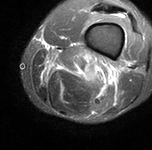
MRI of an extremity soft-tissue mass, one axial slice. Position 19 of 90 along the scan axis. STIR. MR volume resampled by the dataset authors to the PET/CT grid (not the native acquisition matrix). 3.27 mm slice thickness. 152 × 150 image matrix, field of view 148 × 146 mm. Male patient. From the clinical record (not read from this slice): histological type: undifferentiated pleomorphic liposarcoma; grade: high; site of the primary tumour: left thigh.
Structures marked on this image (expert contour drawn on MRI and transferred to this co-registered scan by the dataset authors):
- gross tumour volume including surrounding oedema: bounding box <43,57,117,86> (left, top, right, bottom; pixels)